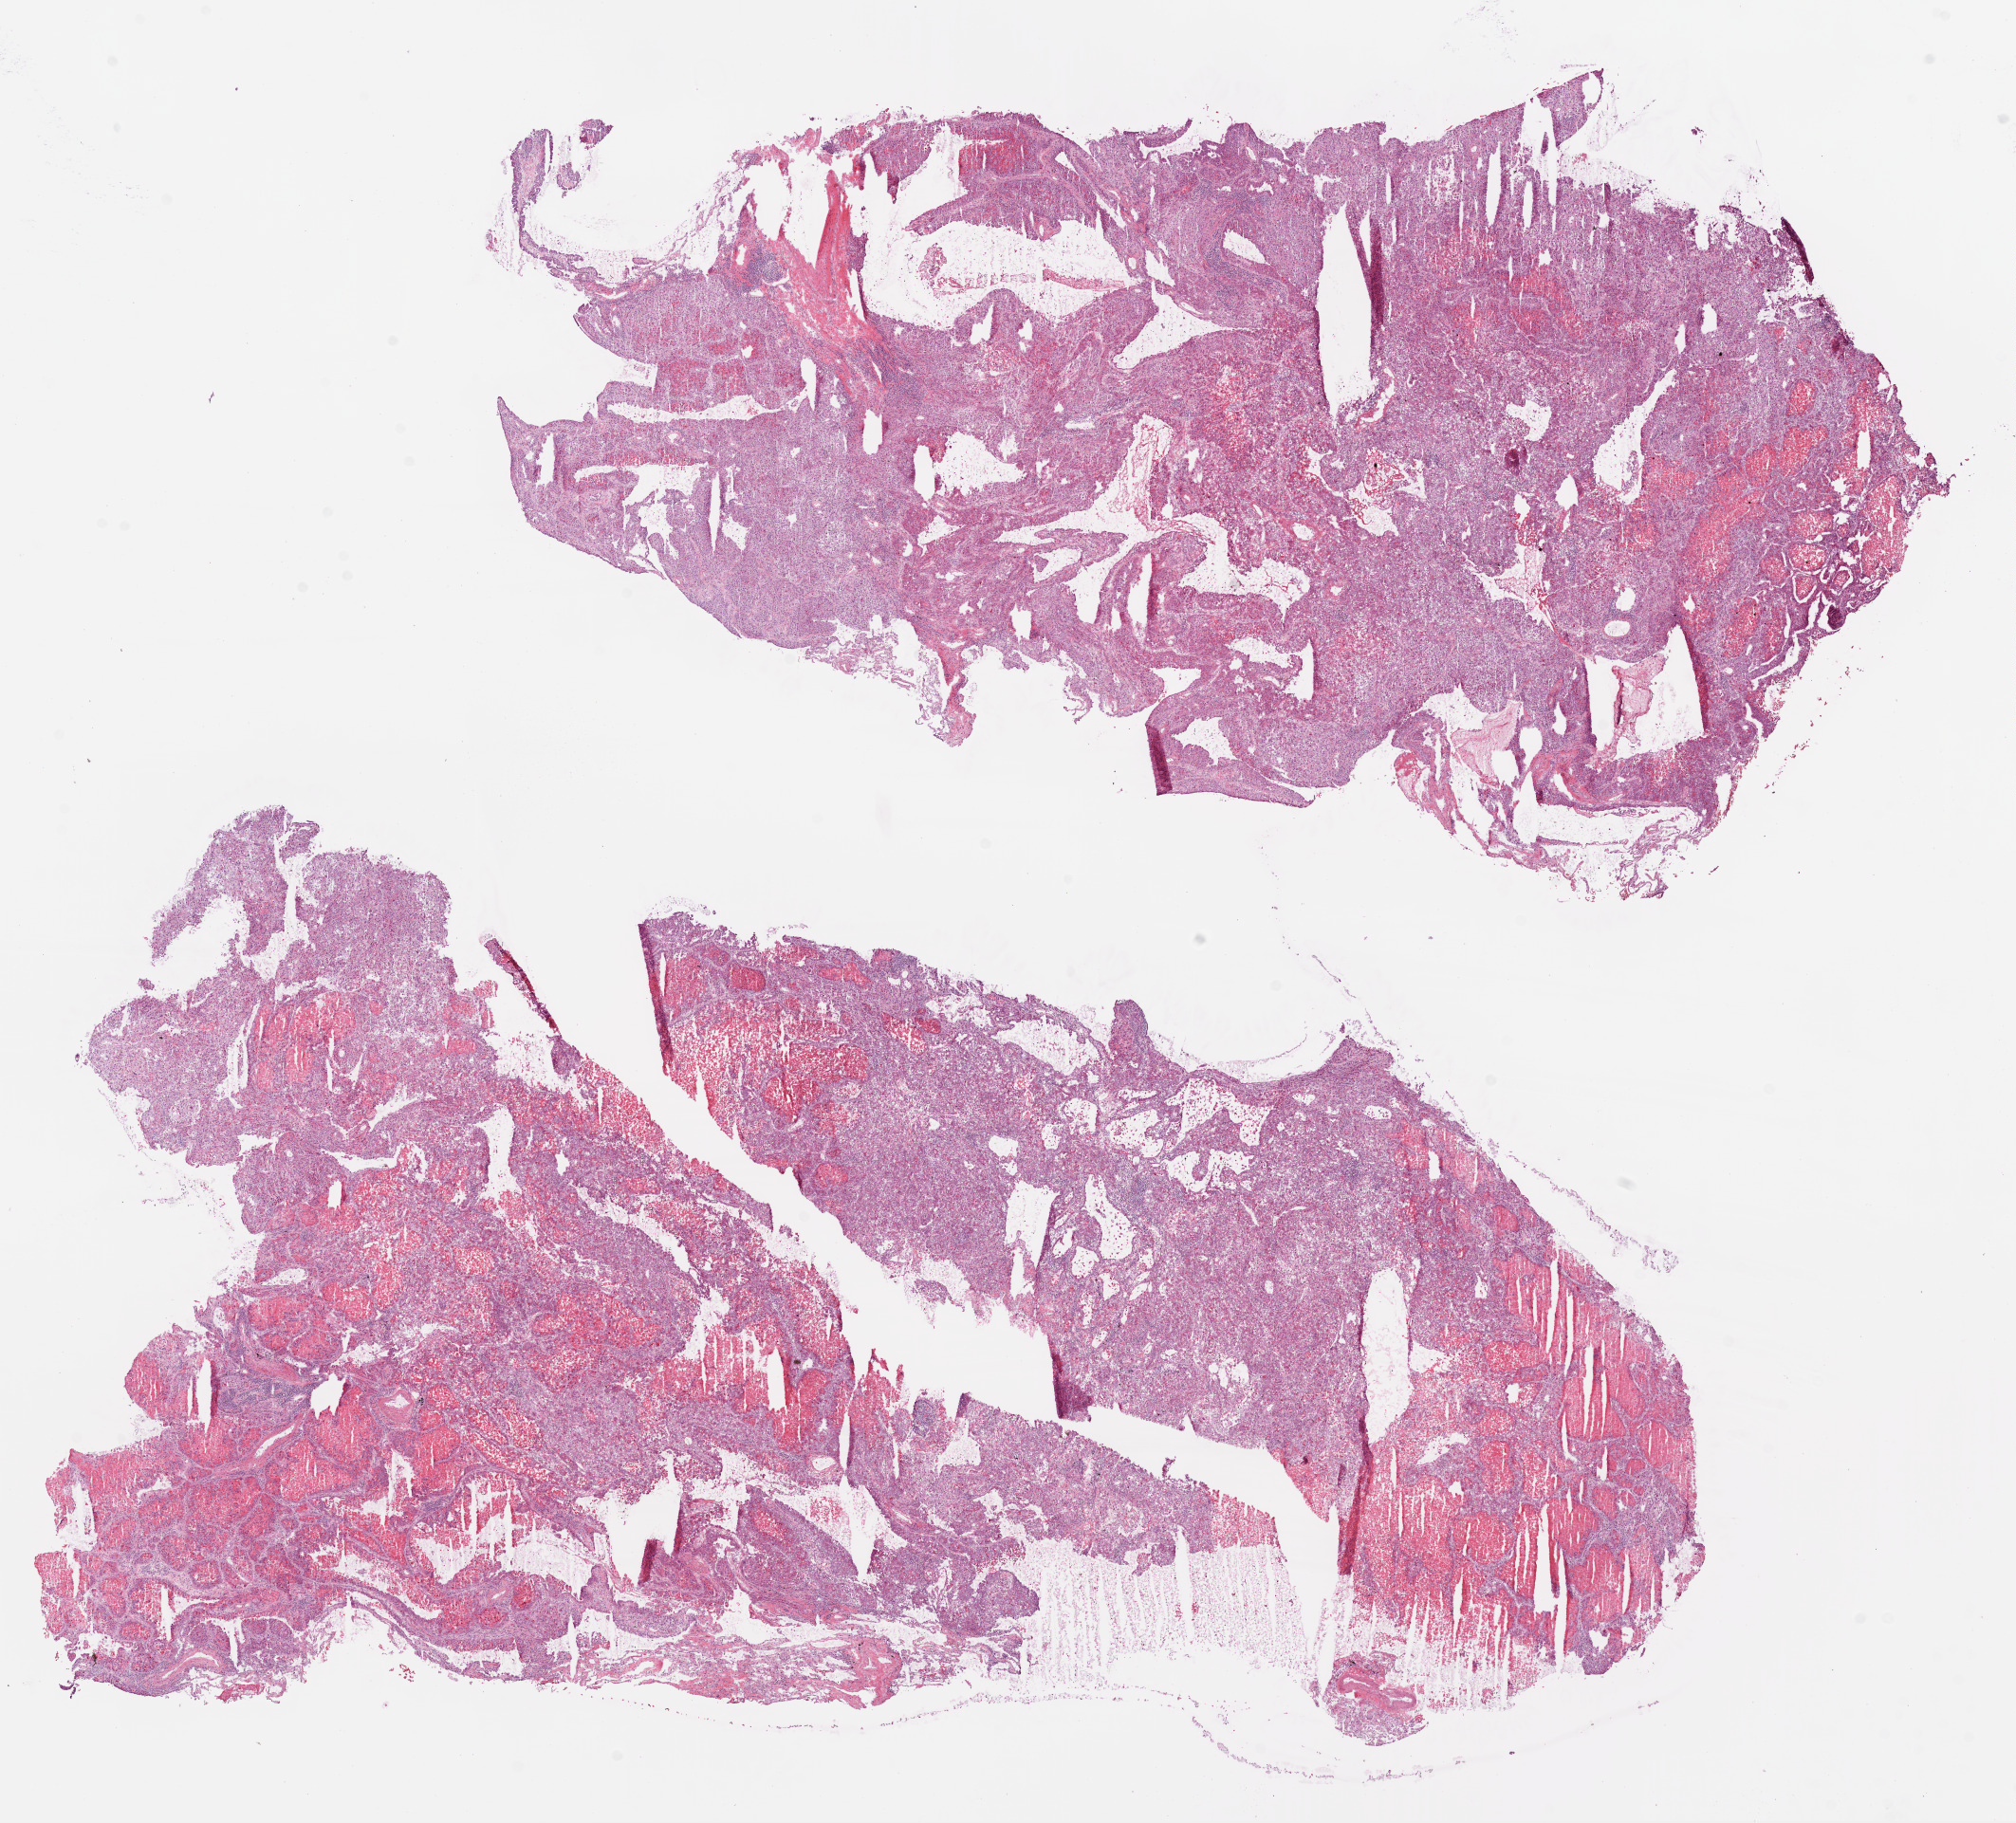
H&E-stained whole-slide image, low-resolution overview of the scanned area, about 17.1 x 15.4 mm (acquisition: 20x scan), frozen section, lung, primary tumour sample. Male, age 59 years at initial diagnosis. Pathologist review of this section (percent, as recorded): tumour cells 40%, tumour nuclei 70%, normal cells 5%, stromal cells 15%, necrosis 40%.
- laterality: left
- AJCC pathologic stage: IIIA (7th edition)
- pathologic diagnosis: Squamous cell carcinoma, NOS (upper lobe, lung)
- TNM: T2a N2 M0